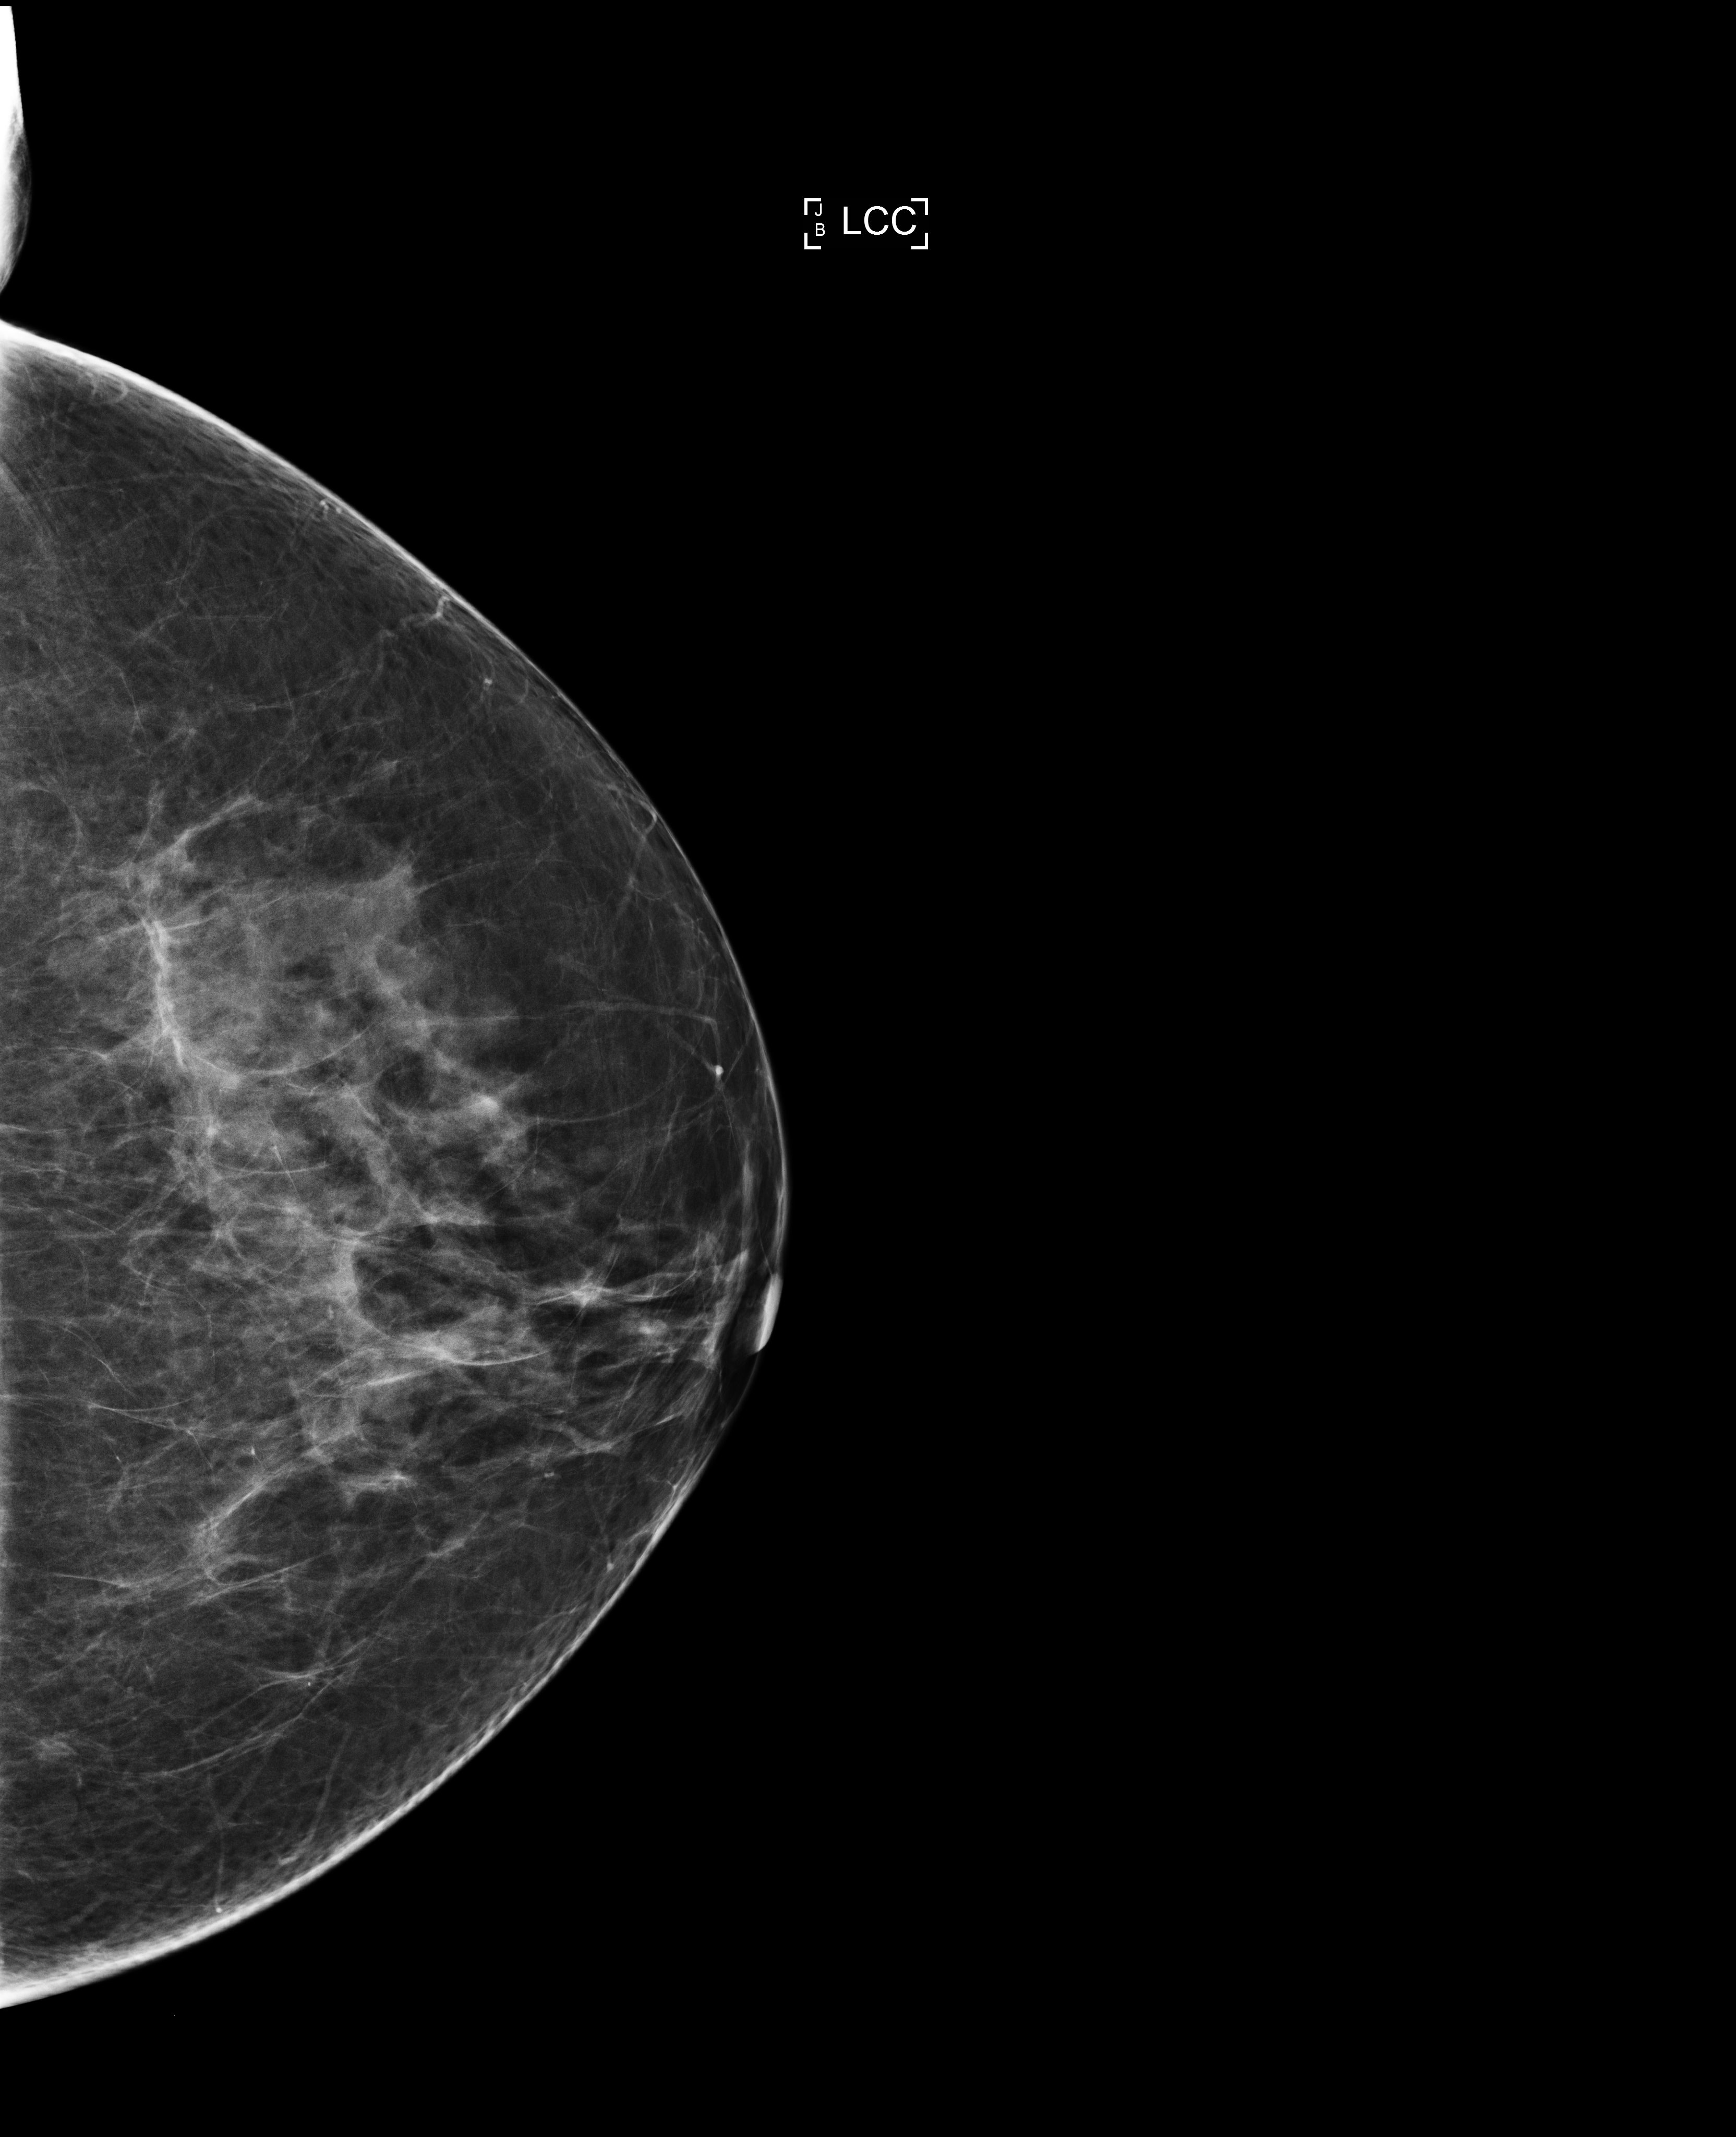
Digital mammogram (FFDM), left breast, craniocaudal (CC) view, screening examination, system: Selenia Dimensions. Female patient, age 55 years.
- breast density at the screening exam (both breasts): heterogeneously dense (BI-RADS density category c)
- final BI-RADS category for the screening round (tomosynthesis exam, both breasts): category 1
- recall: no recall after this screen